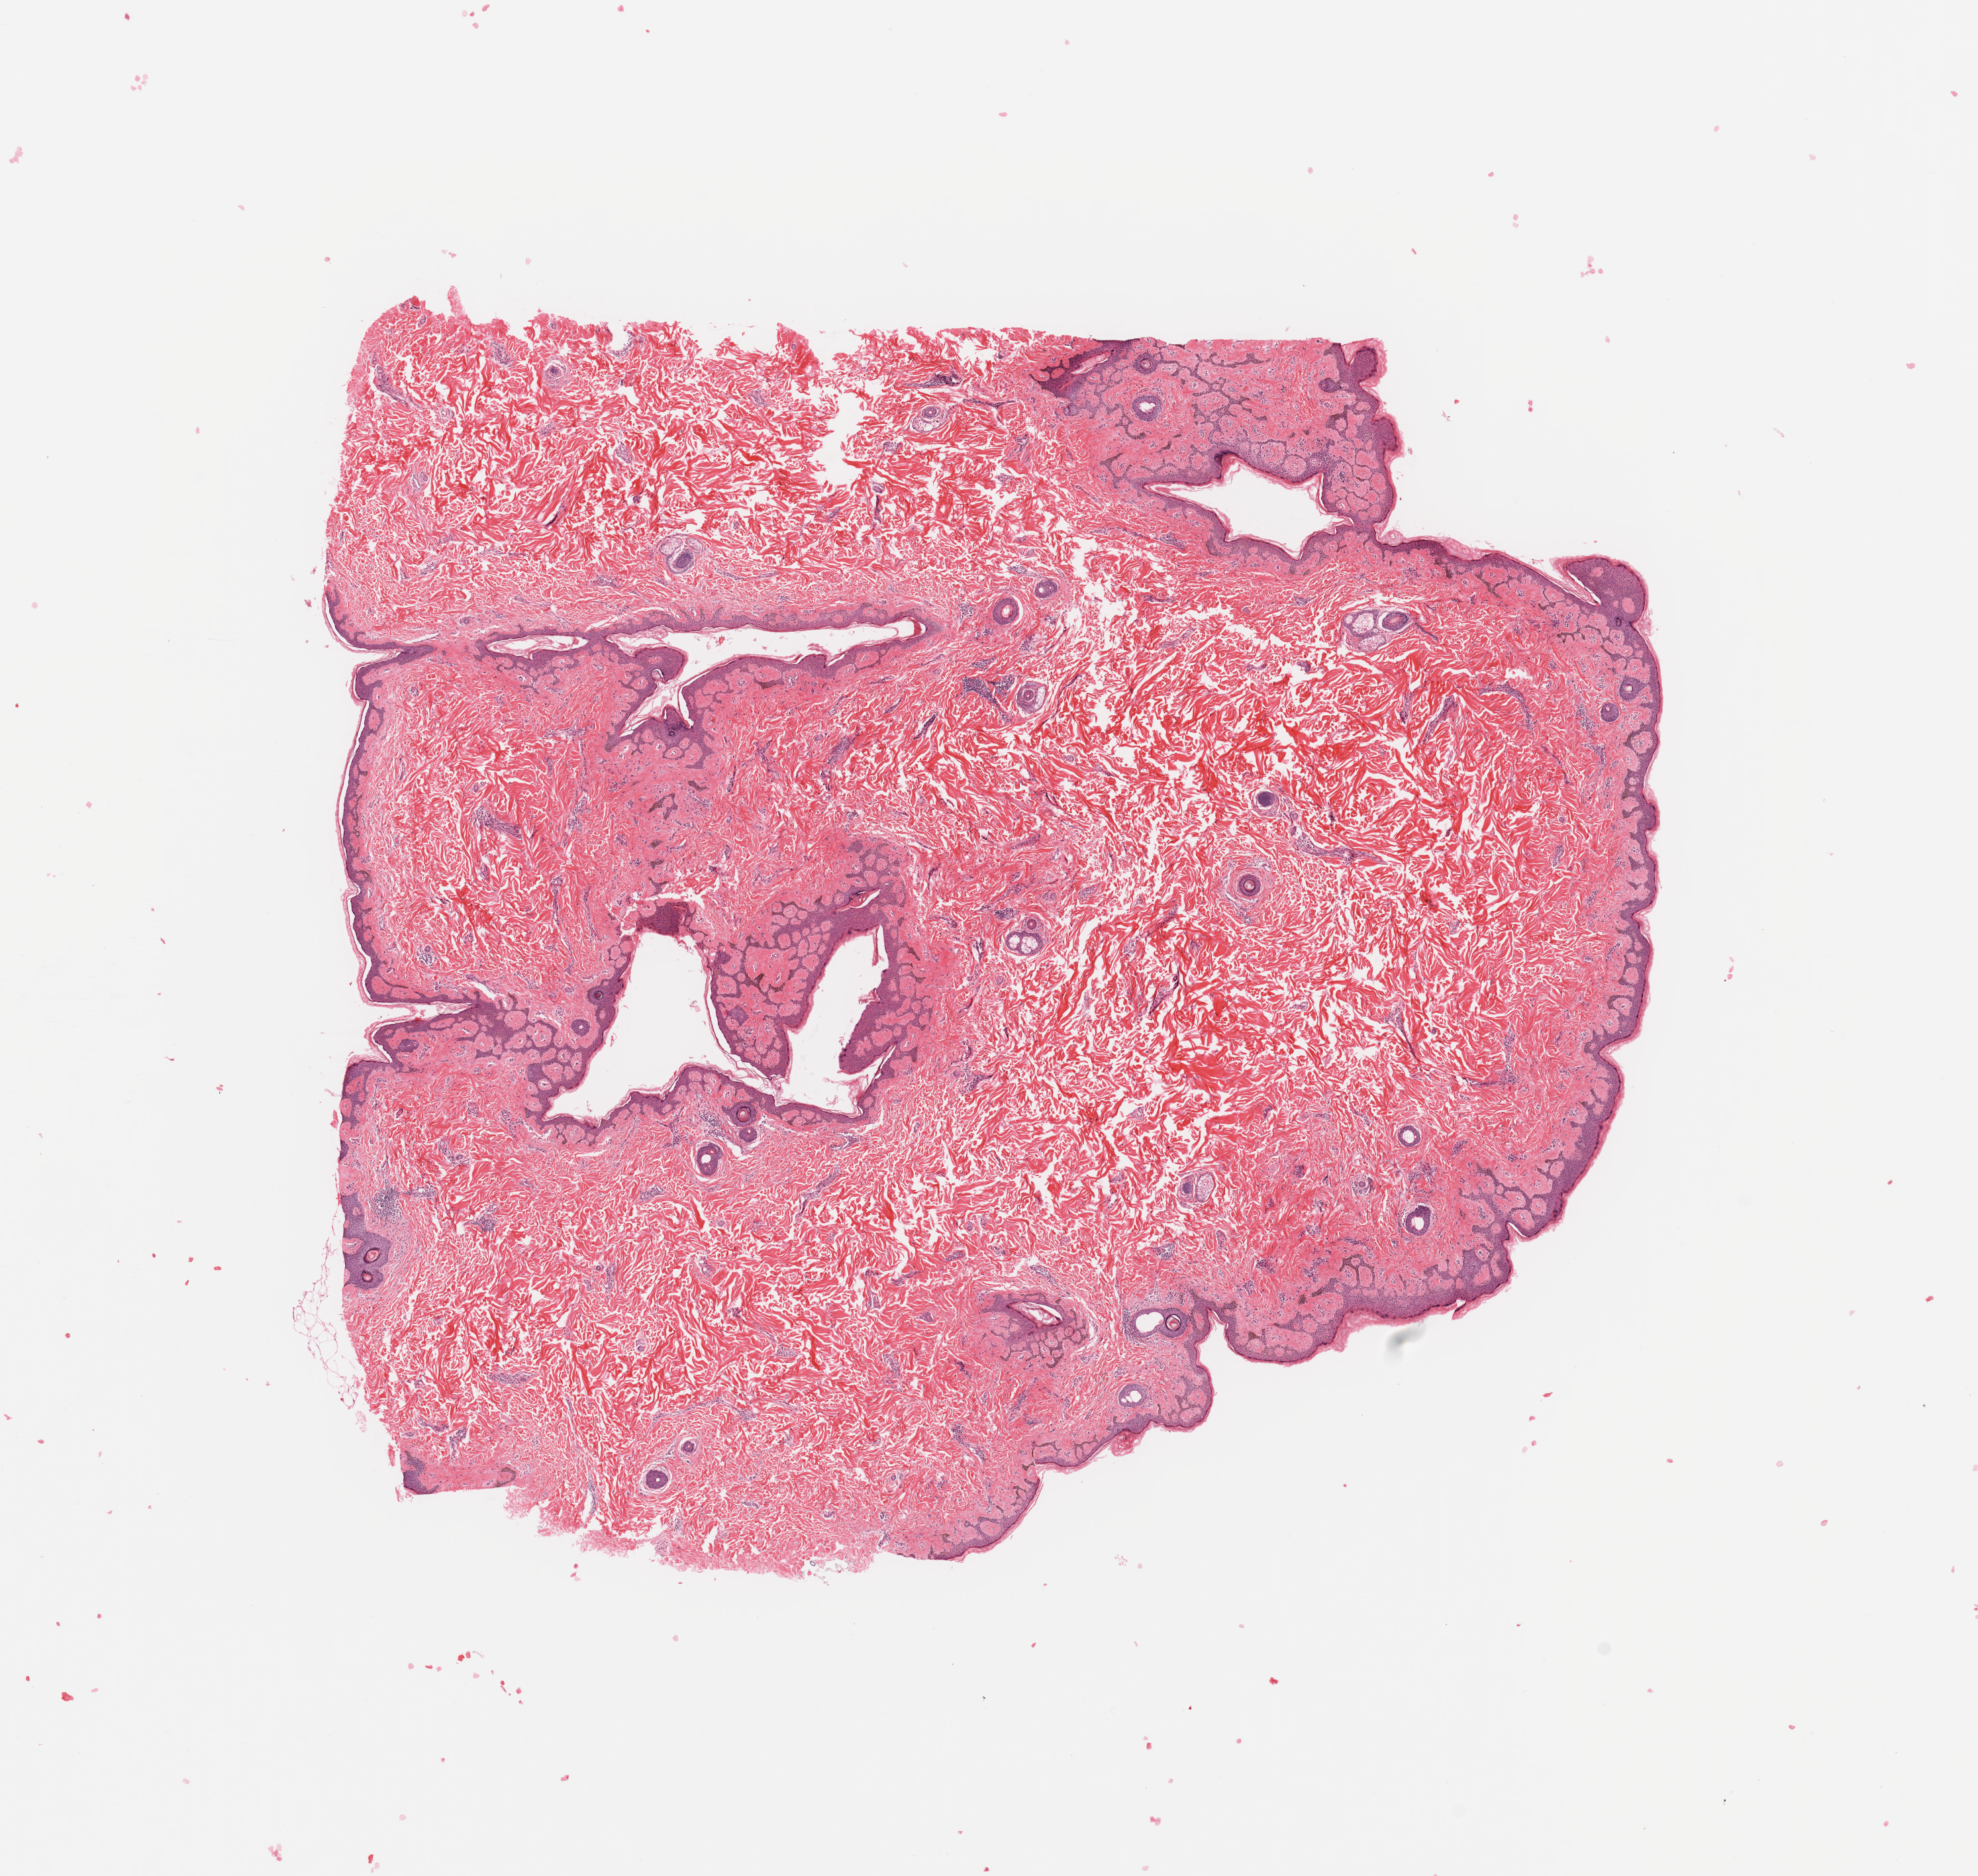
Whole-slide histology image, H&E-stained, low-resolution overview of the scanned area, about 11.8 x 11.2 mm; normal (non-tumour) tissue (melanoma cohort); sampled site not recorded. Female, 66 y/o.
This section: normal (non-tumour) tissue from the same patient. Patient diagnosis (cohort enrolment): cutaneous melanoma (skin).